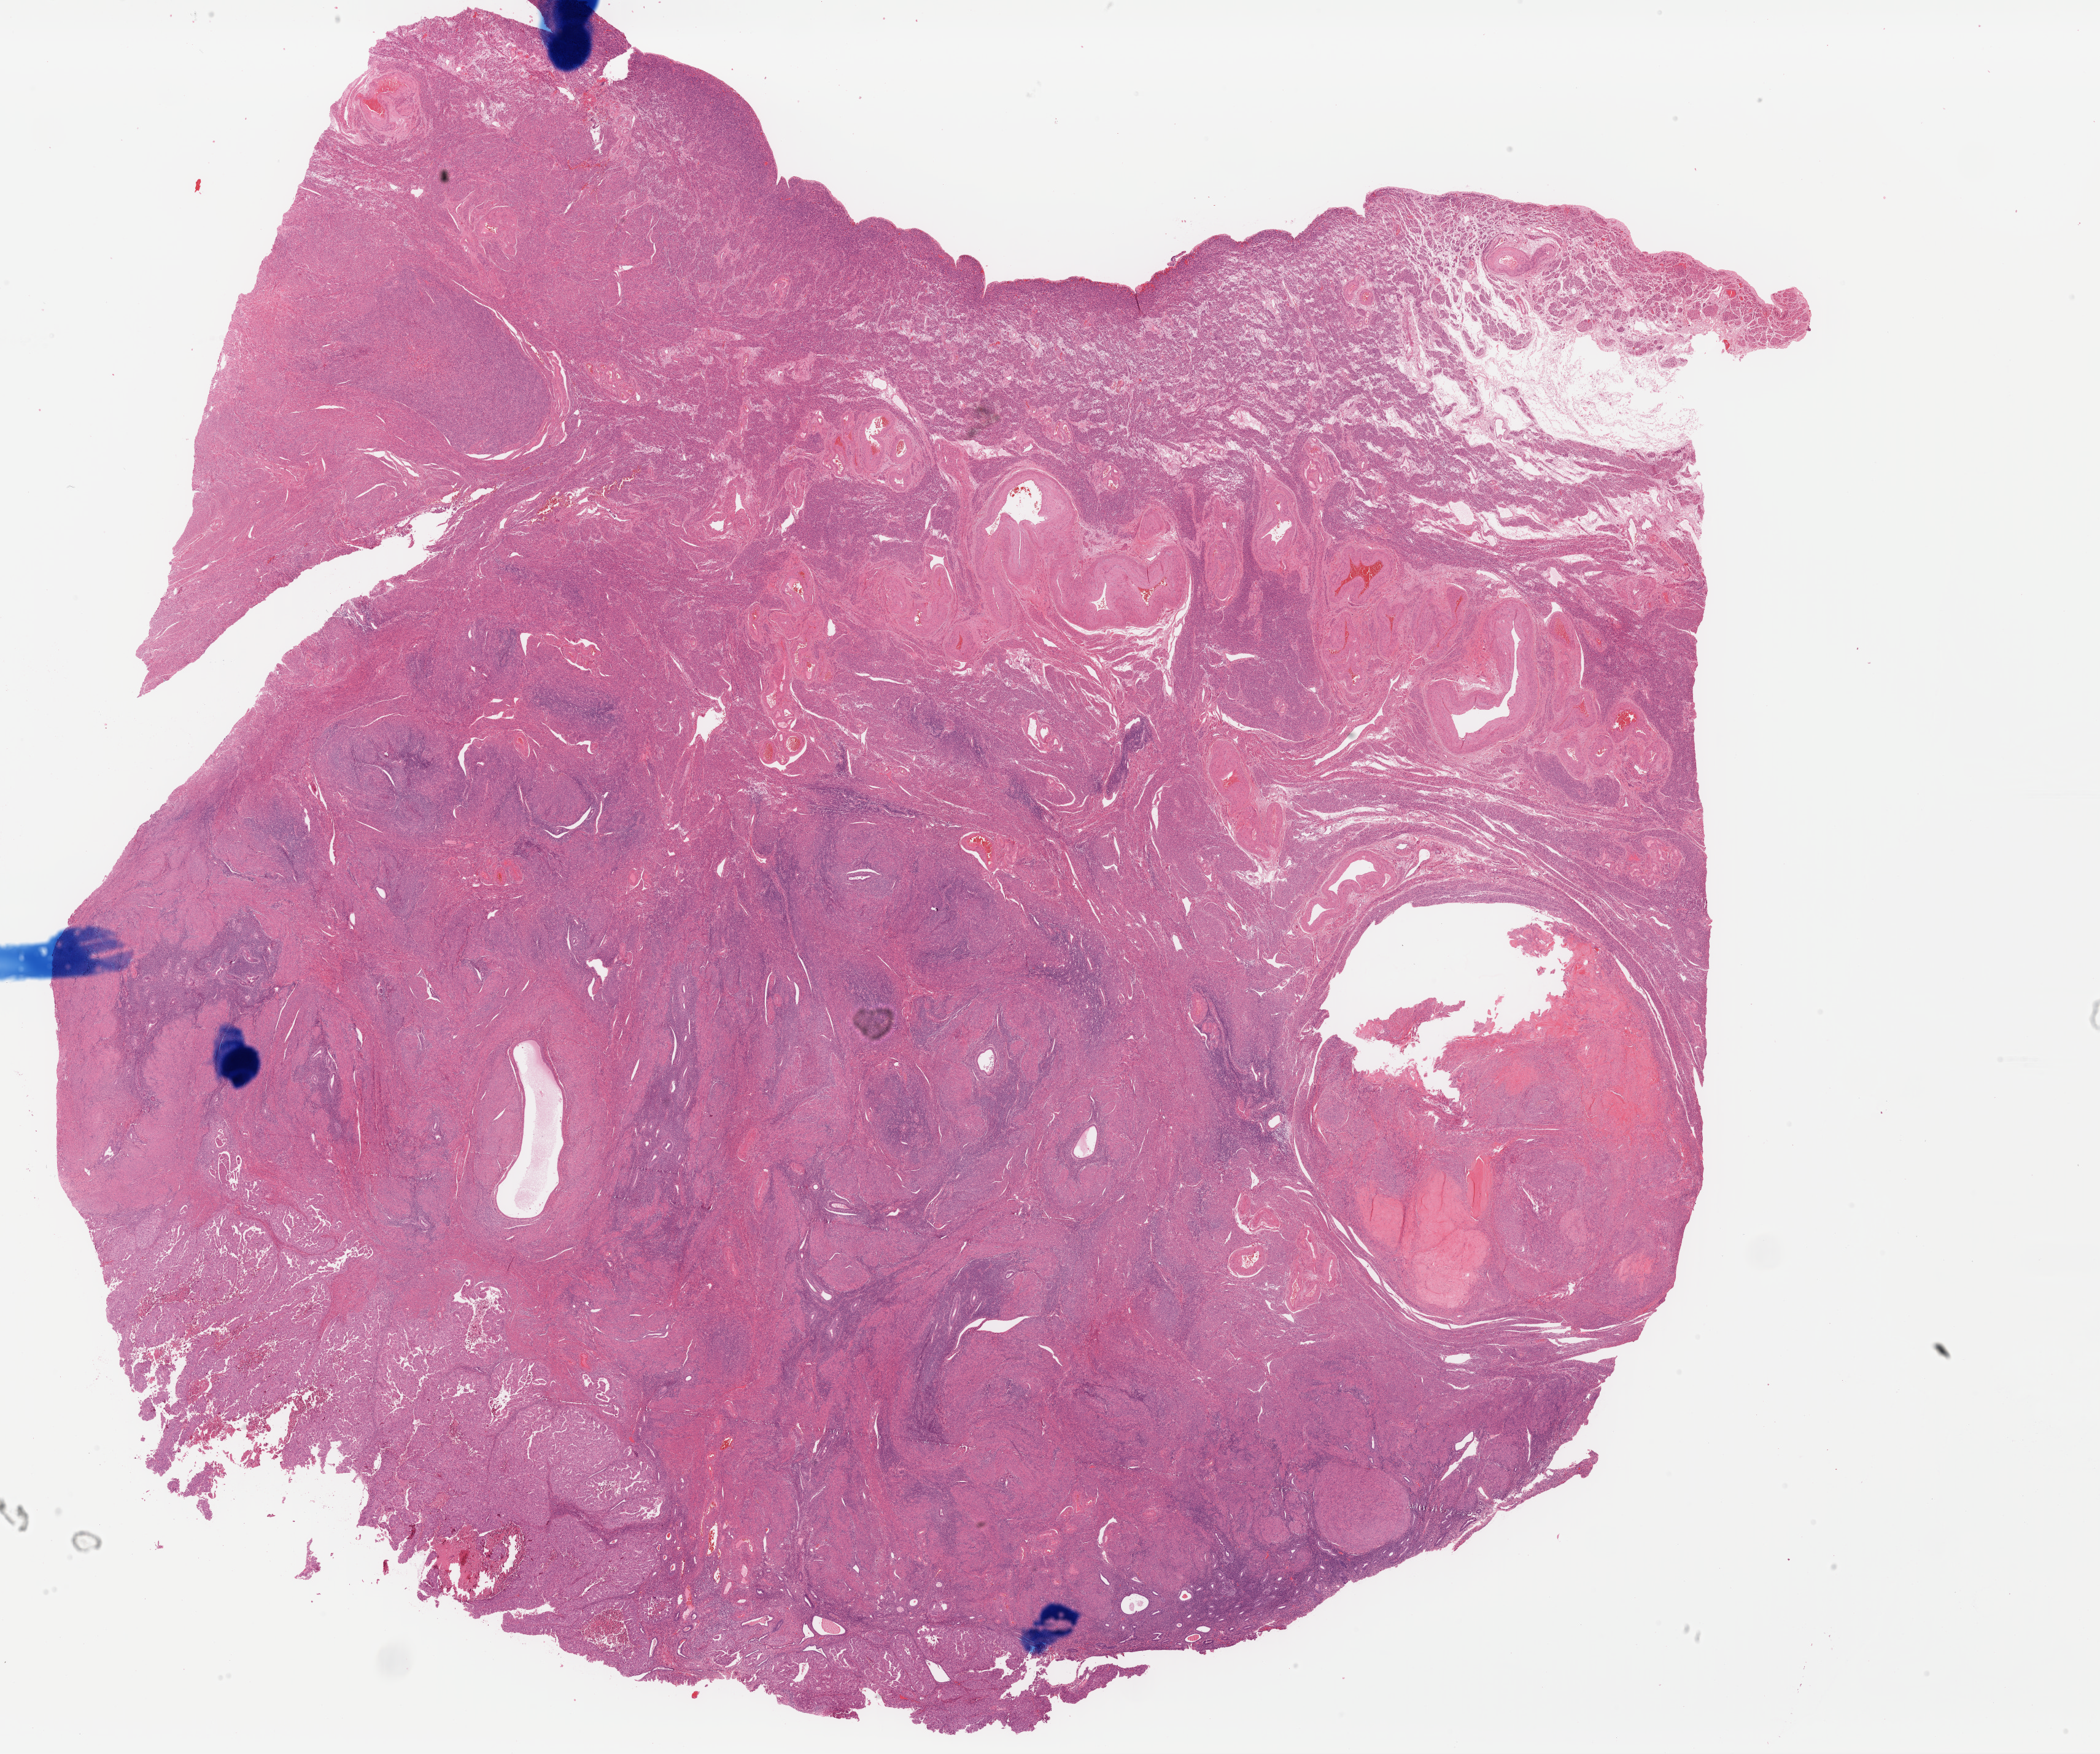
Hematoxylin and eosin (H&E) stained whole-slide image — low-resolution overview of the scanned area, about 27.0 x 22.6 mm (acquisition: 40x scan). Formalin-fixed paraffin-embedded (FFPE) diagnostic section. Primary tumour sample from the uterus. Female patient; age at initial diagnosis 64 years. Histologic grade: G3 (poorly differentiated).
• lymph nodes positive (case pathology): 0 of 6 examined
• pathologic diagnosis: Serous cystadenocarcinoma, NOS (endometrium)
• FIGO stage: II